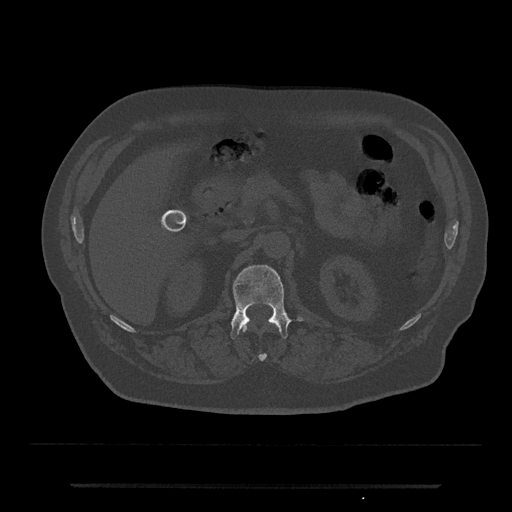
CT including the spine, one axial slice. Position 550 of 797 along the scan axis. Reconstruction kernel Br40s/3. Bone window (W 1800 / L 400 HU). 512 × 512 image matrix, field of view 434 × 434 mm. Male patient, age 80 years. From the clinical record (not read from this slice): primary cancer: prostate; vertebrae with lytic lesions (as recorded): L1, T11.
Outlined on this slice (semi-automatic segmentation, software-assisted and operator-edited):
- L1 vertebra: bounding box [x1, y1, x2, y2] px = [230, 265, 304, 339]
- T12 vertebra: [242, 325, 279, 361]